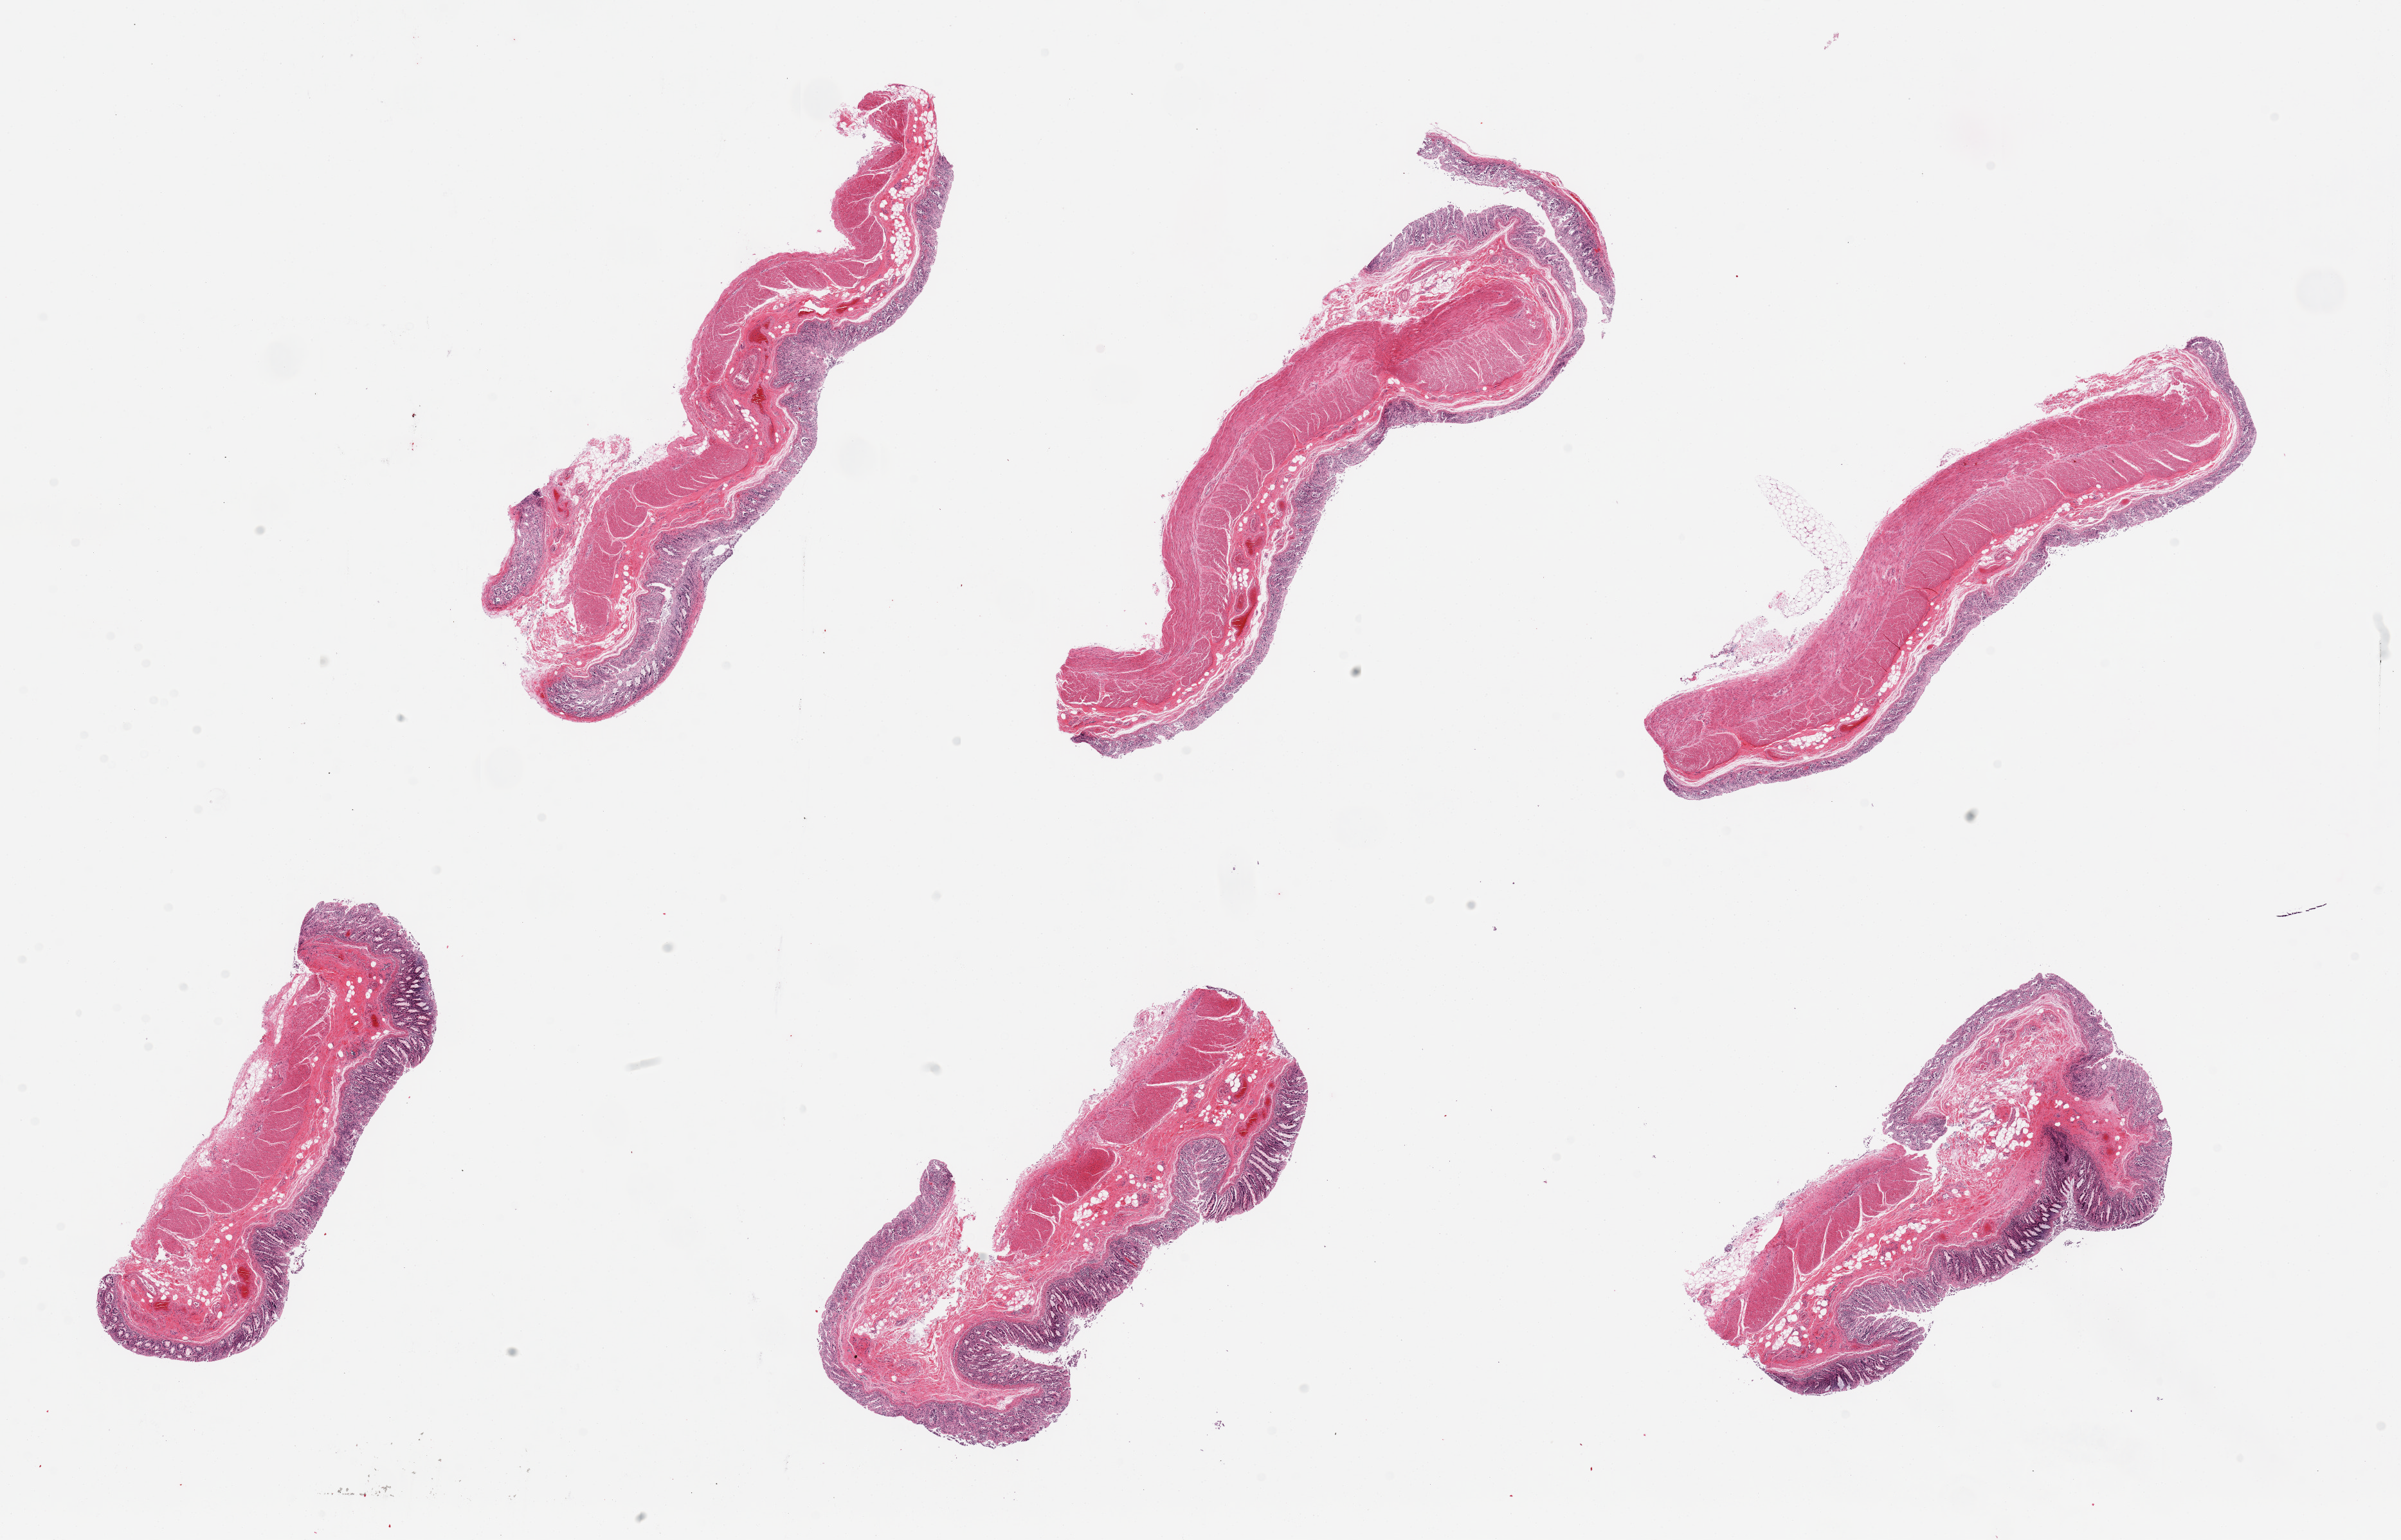
Digitized haematoxylin and eosin-stained section — shown as a low-resolution overview of the whole scanned area (about 29.5 x 18.9 mm). PAXgene-fixed paraffin-embedded (PFPE) section. Sampled site (target tissue): transverse colon. Tissue donor sample. Donor sex: male.
- review note (as recorded): 6 pieces; mucosa=3 (focally=2); muscle=1